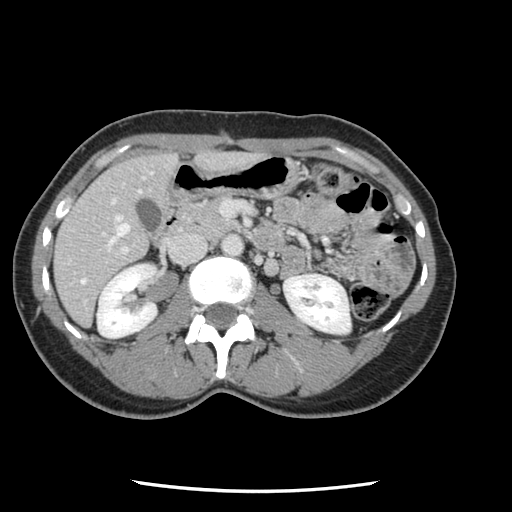
Contrast-enhanced abdominal CT, one axial slice; slice 45 of 134 in the series (ordered by position); intravenous contrast given; soft-tissue window (W 400 / L 40 HU); 2.5 mm slice thickness; 512 × 512 image matrix. Female patient, age 43 years. From the clinical record (not read from this slice): diagnosis: colorectal cancer liver metastases, imaged before liver resection; multiple liver metastases: yes; largest metastasis: 3.4 cm; chemotherapy before resection: no.
Outlined on this slice (outlined manually by an expert reader):
- hepatic veins: box from (x=81, y=191) to (x=141, y=284) px
- liver: (x=56, y=154)–(x=177, y=324)
- planned liver remnant (the part of the liver to remain after resection): (x=56, y=154)–(x=177, y=324)
- portal vein (with intrahepatic branches): (x=68, y=201)–(x=250, y=304)